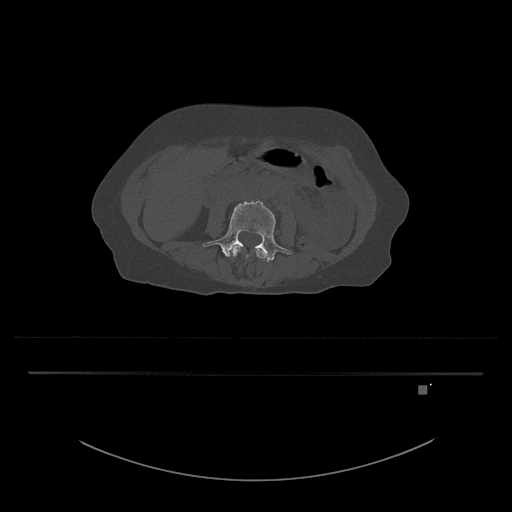
CT including the spine, one axial slice; slice 378 of 797 in the series (ordered by position); reconstruction kernel Br40s/3; 120 kVp; bone window (W 1800 / L 400 HU); 0.5 mm slice thickness; 512 × 512 image matrix, field of view 500 × 500 mm. Female patient, age 57 years. Case-level facts recorded for this patient, not image findings: primary cancer: cervical.
Structures marked on this image (semi-automatic segmentation, software-assisted and operator-edited):
- L3 vertebra: box from (x=231, y=246) to (x=267, y=259) px
- L4 vertebra: (x=202, y=200)–(x=293, y=263)